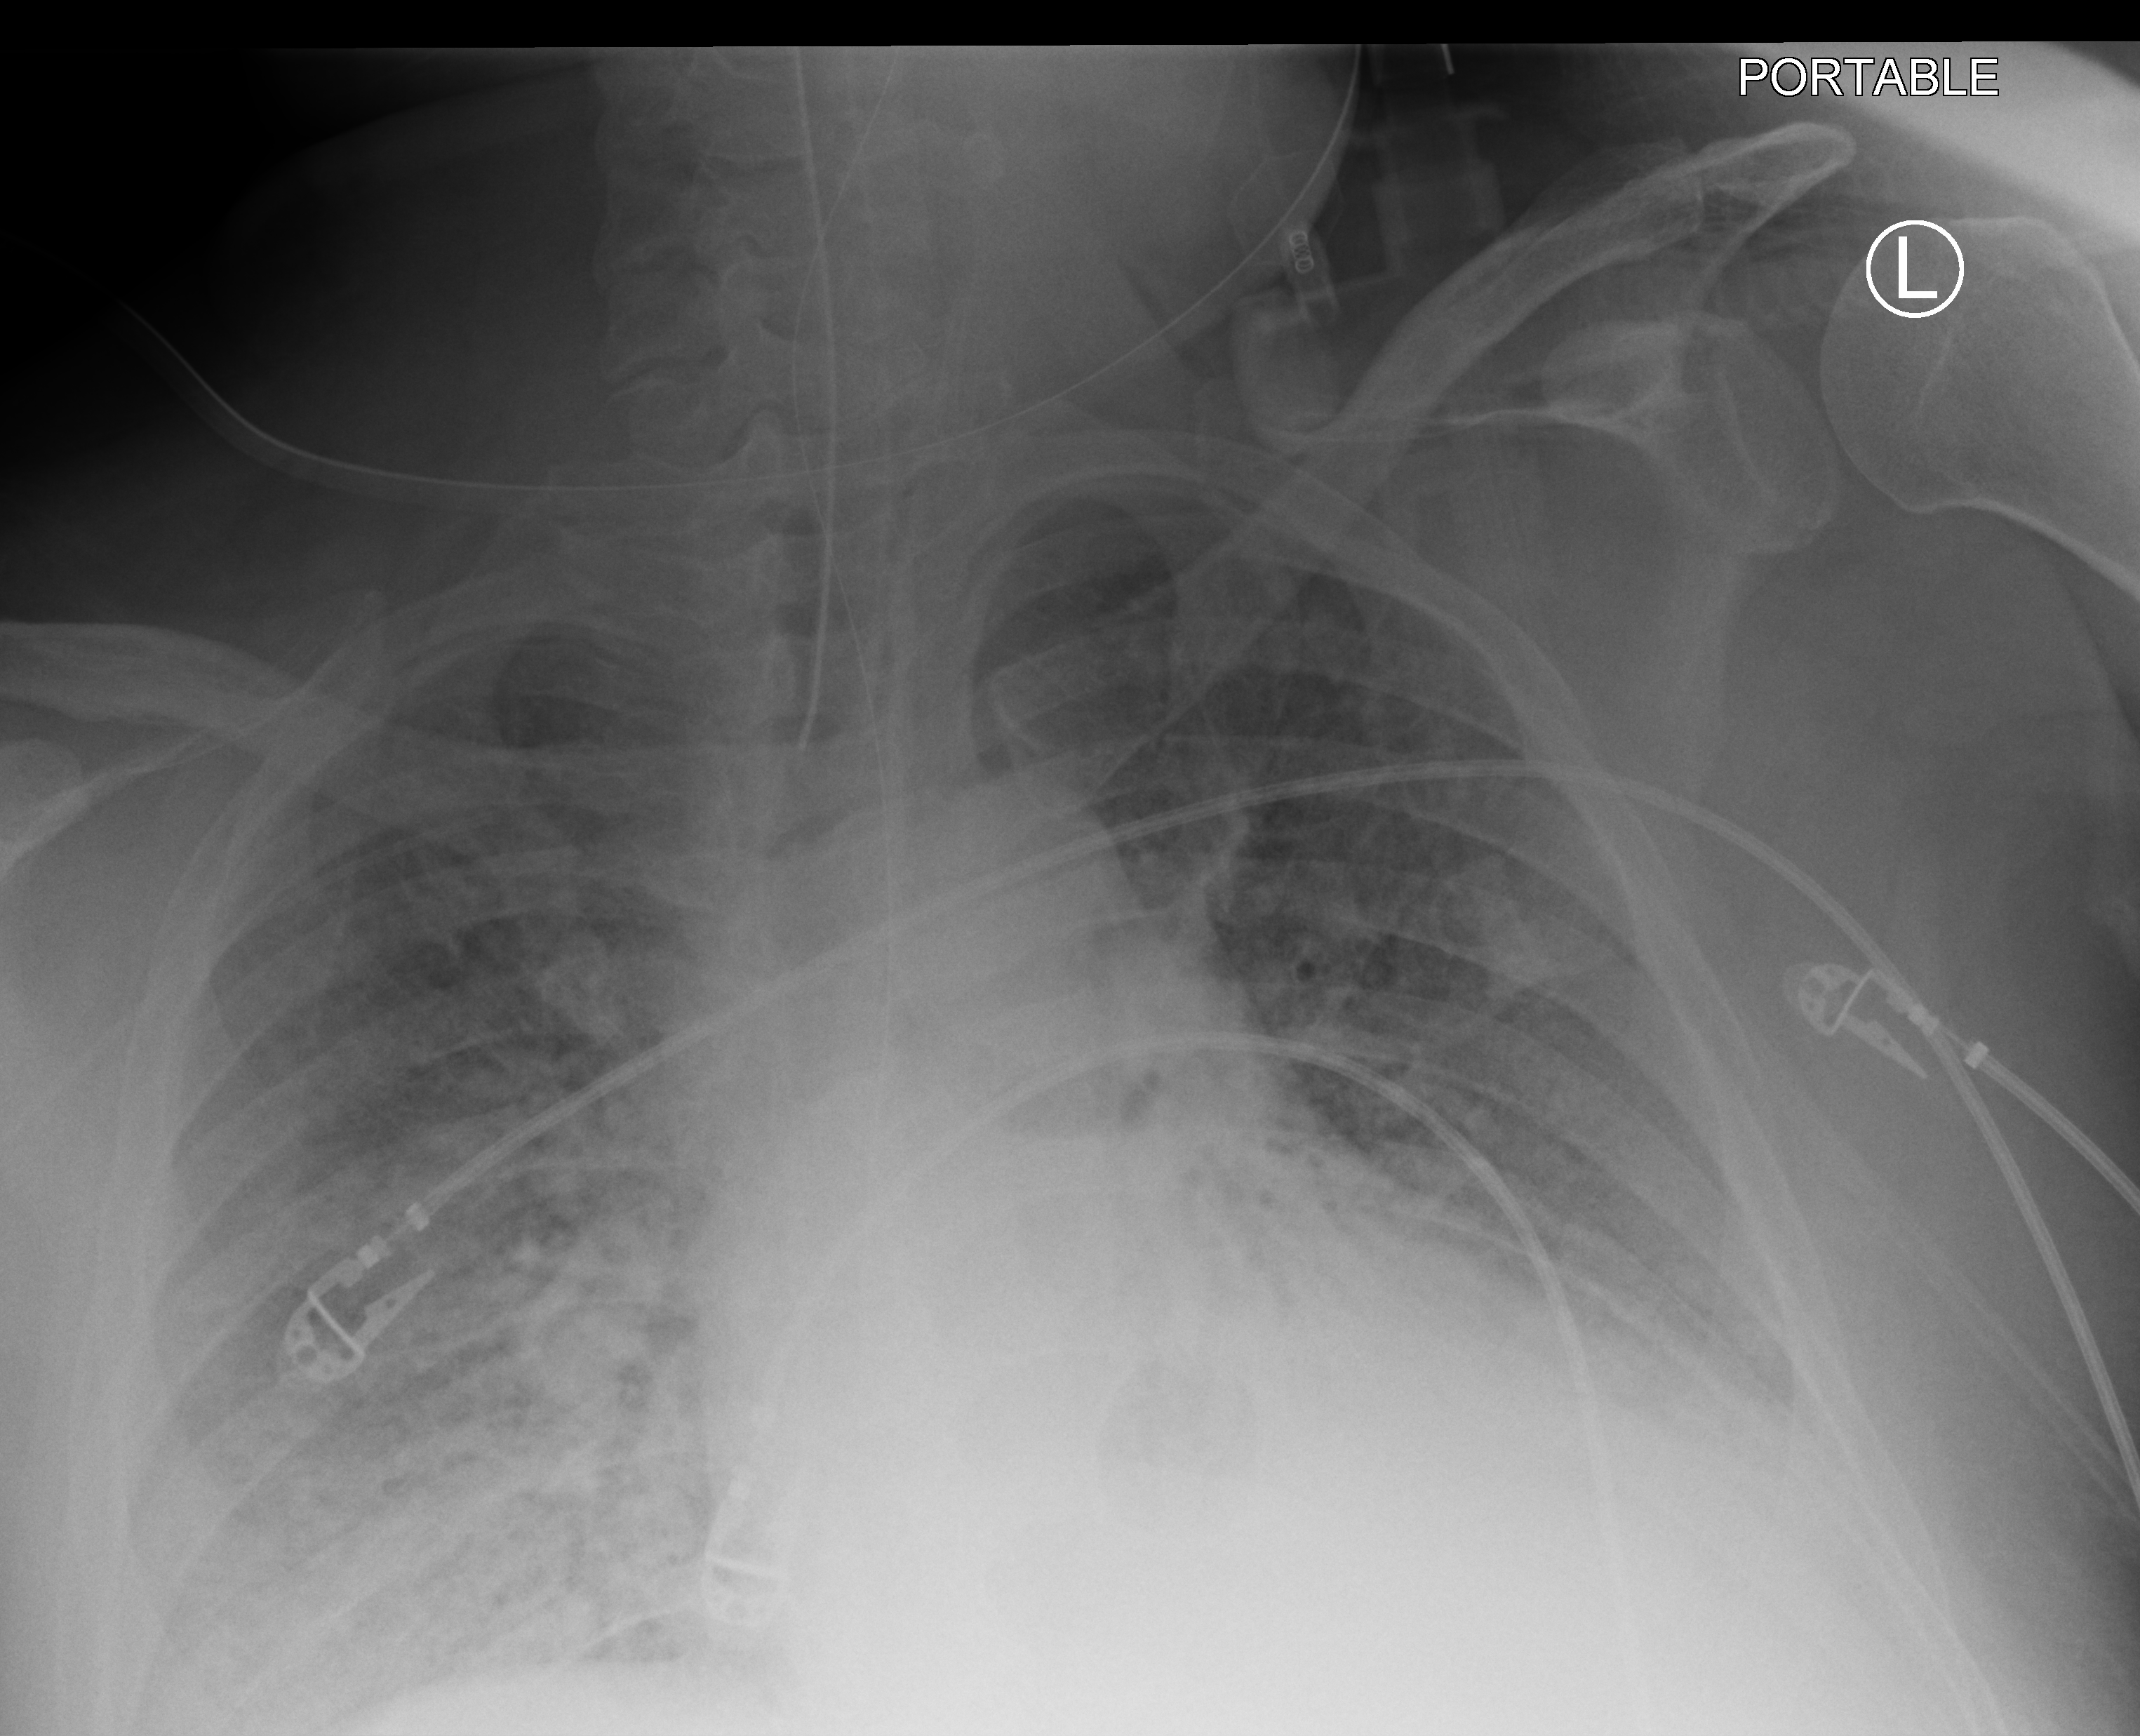
Portable chest radiograph, anteroposterior (AP) projection. Adult patient hospitalised with COVID-19, age 18–59 years.
Admission-level facts for this patient (not findings on this image; timing relative to this image not recorded): mechanically ventilated during this hospital stay: yes.